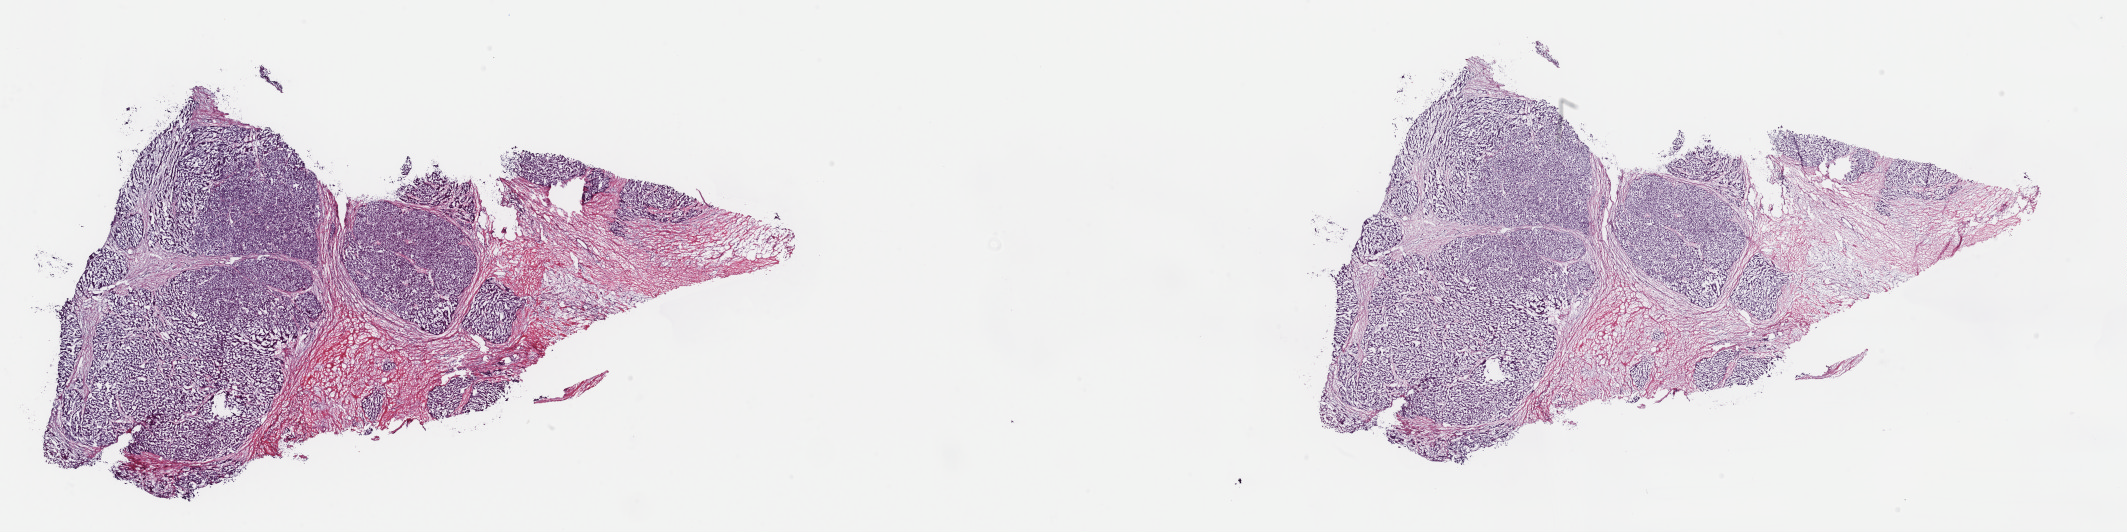
Whole-slide histology image, H&E, shown as a low-resolution overview of the whole scanned area (about 33.6 x 8.4 mm), frozen section from the top of the tissue portion, sample: primary tumour, liver. Patient: male, age at initial diagnosis 54 years. Histologic grade: G2 (moderately differentiated). Pathologist review of this section (percent, as recorded): tumour cells 75%, tumour nuclei 75%, normal cells 0%, stromal cells 25%, necrosis 0%. Inflammatory infiltration, as recorded: lymphocyte infiltration 4%, monocyte infiltration 1%, neutrophil infiltration 1%.
TNM: T3 N0 M0. Histologic diagnosis: Hepatocellular carcinoma, NOS. AJCC pathologic stage: IIIA (7th edition).